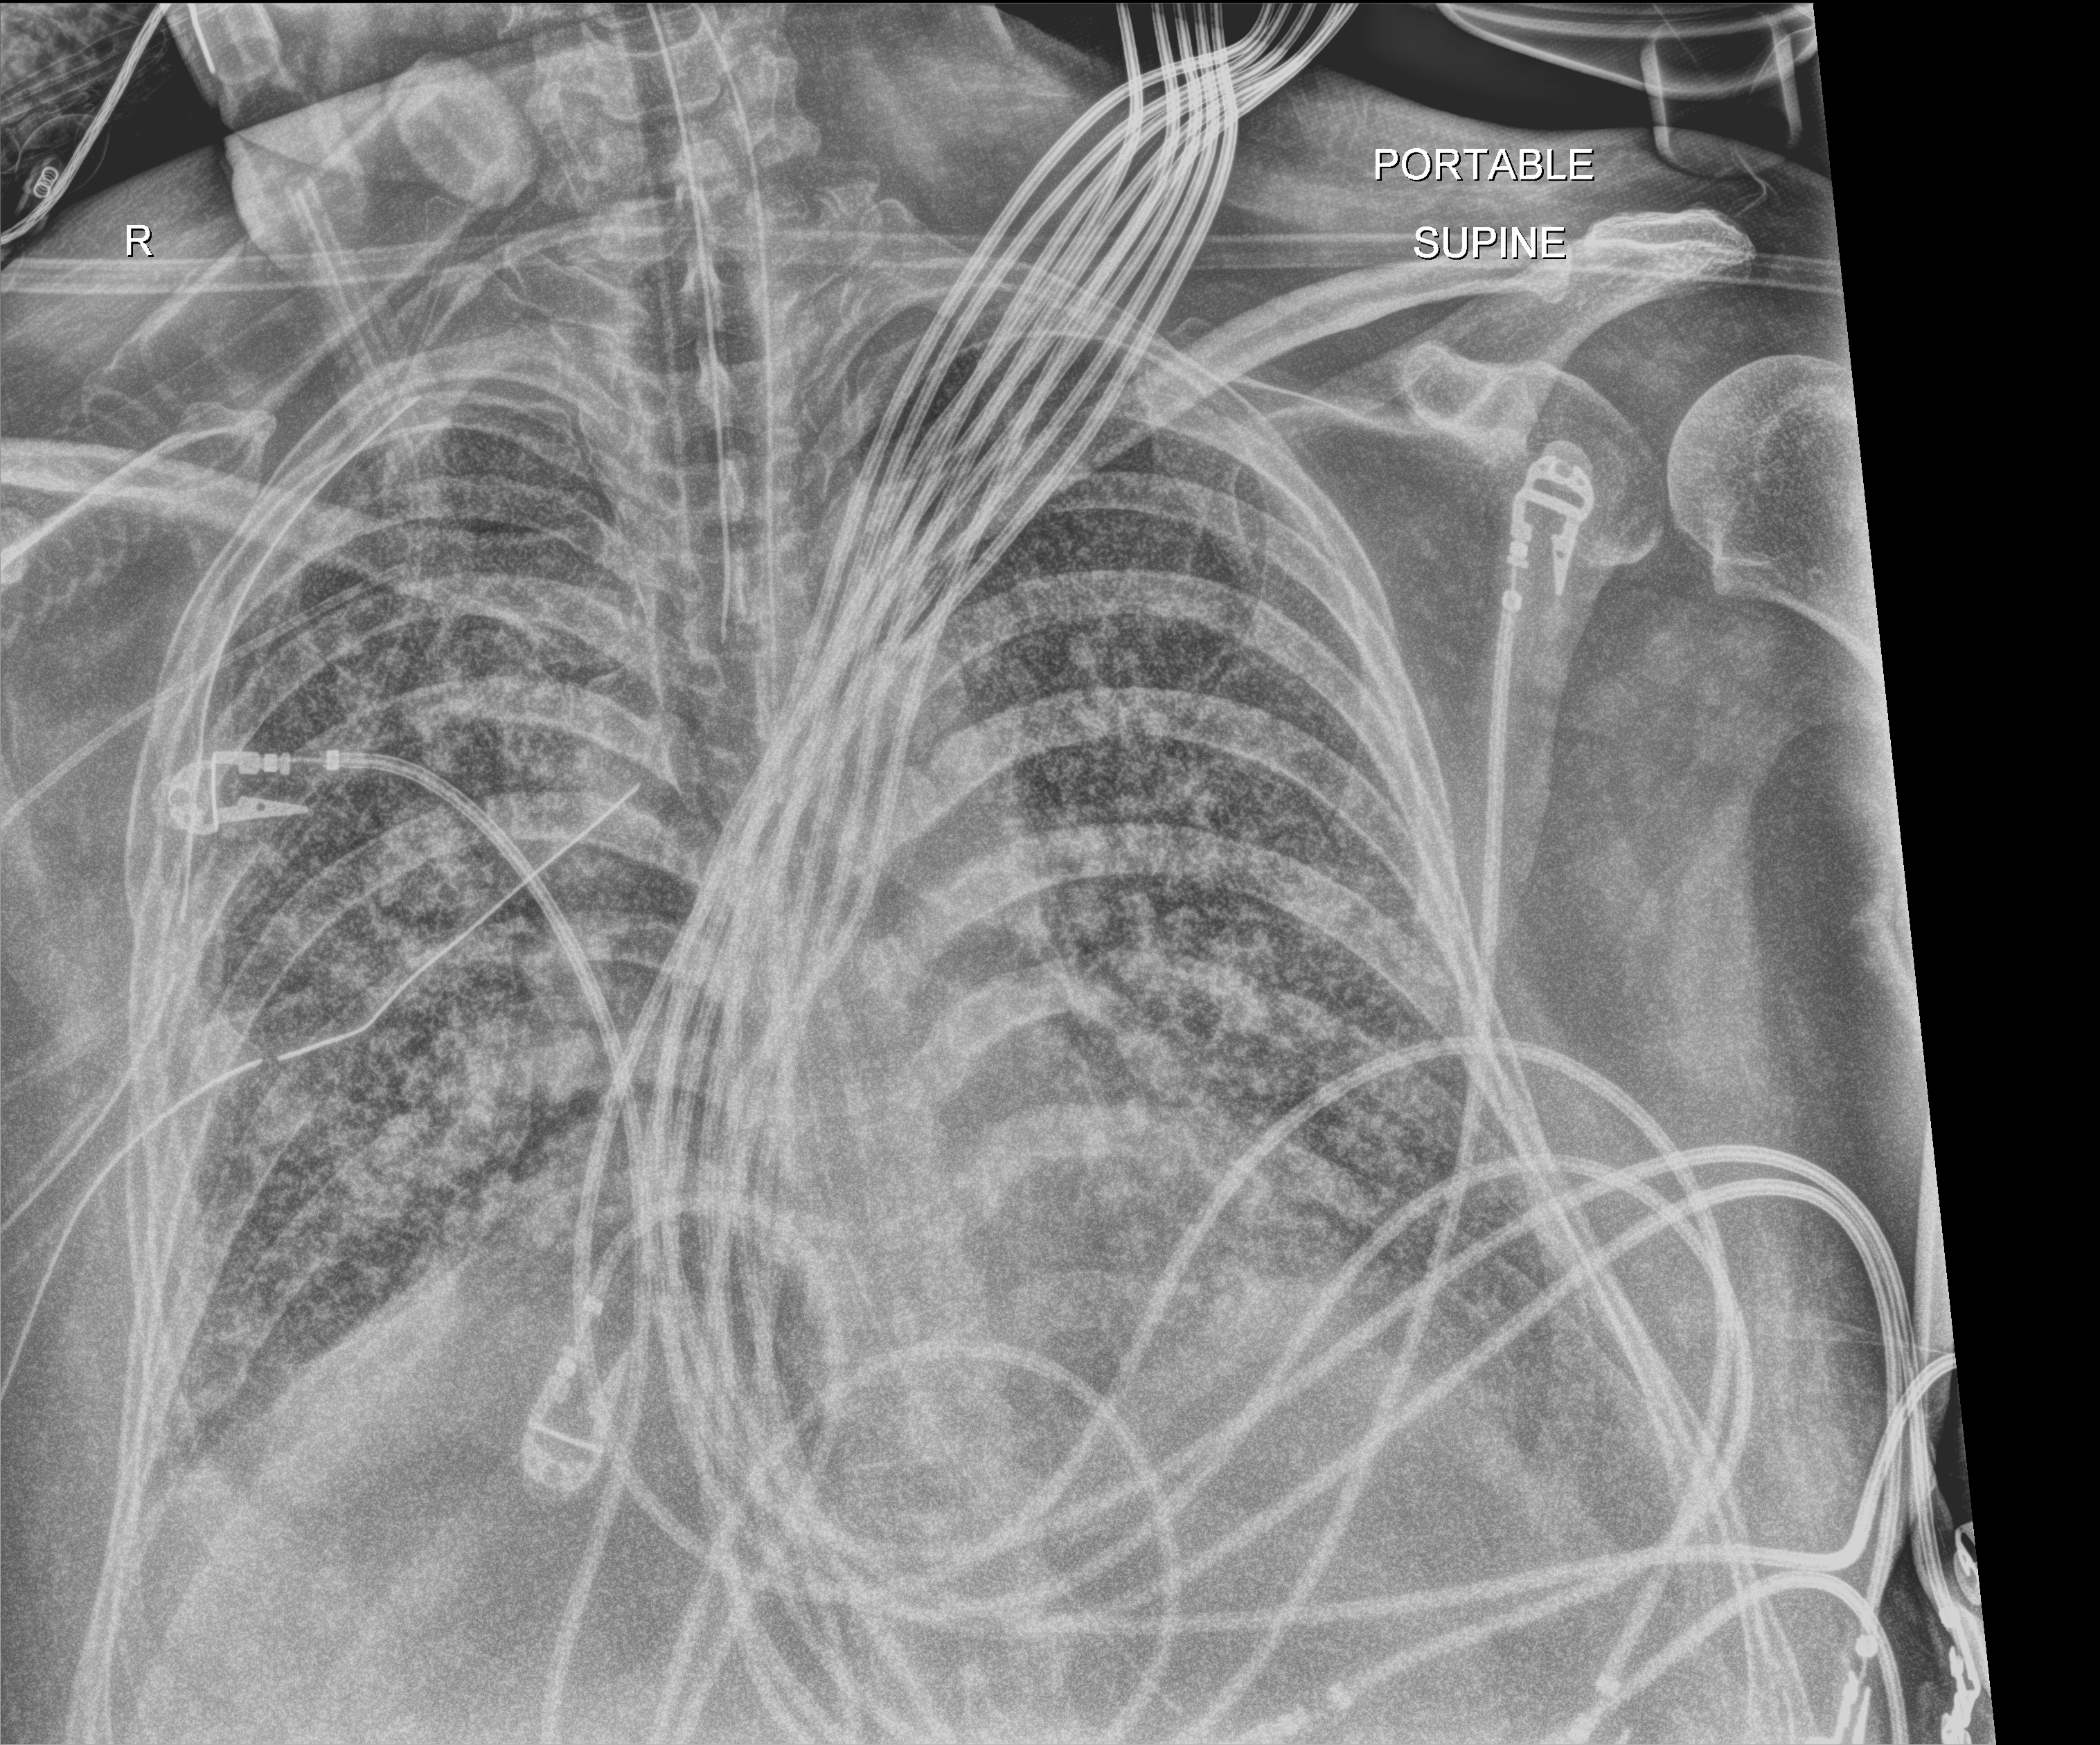
Portable chest radiograph, anteroposterior (AP) projection. Adult patient hospitalised with COVID-19, age 18–59 years.
From the hospital-stay record, not from the radiograph (when in the stay this image was taken is not recorded):
- chronic kidney disease (admission record): no
- hypertension (admission record): no
- mechanically ventilated during this hospital stay: yes